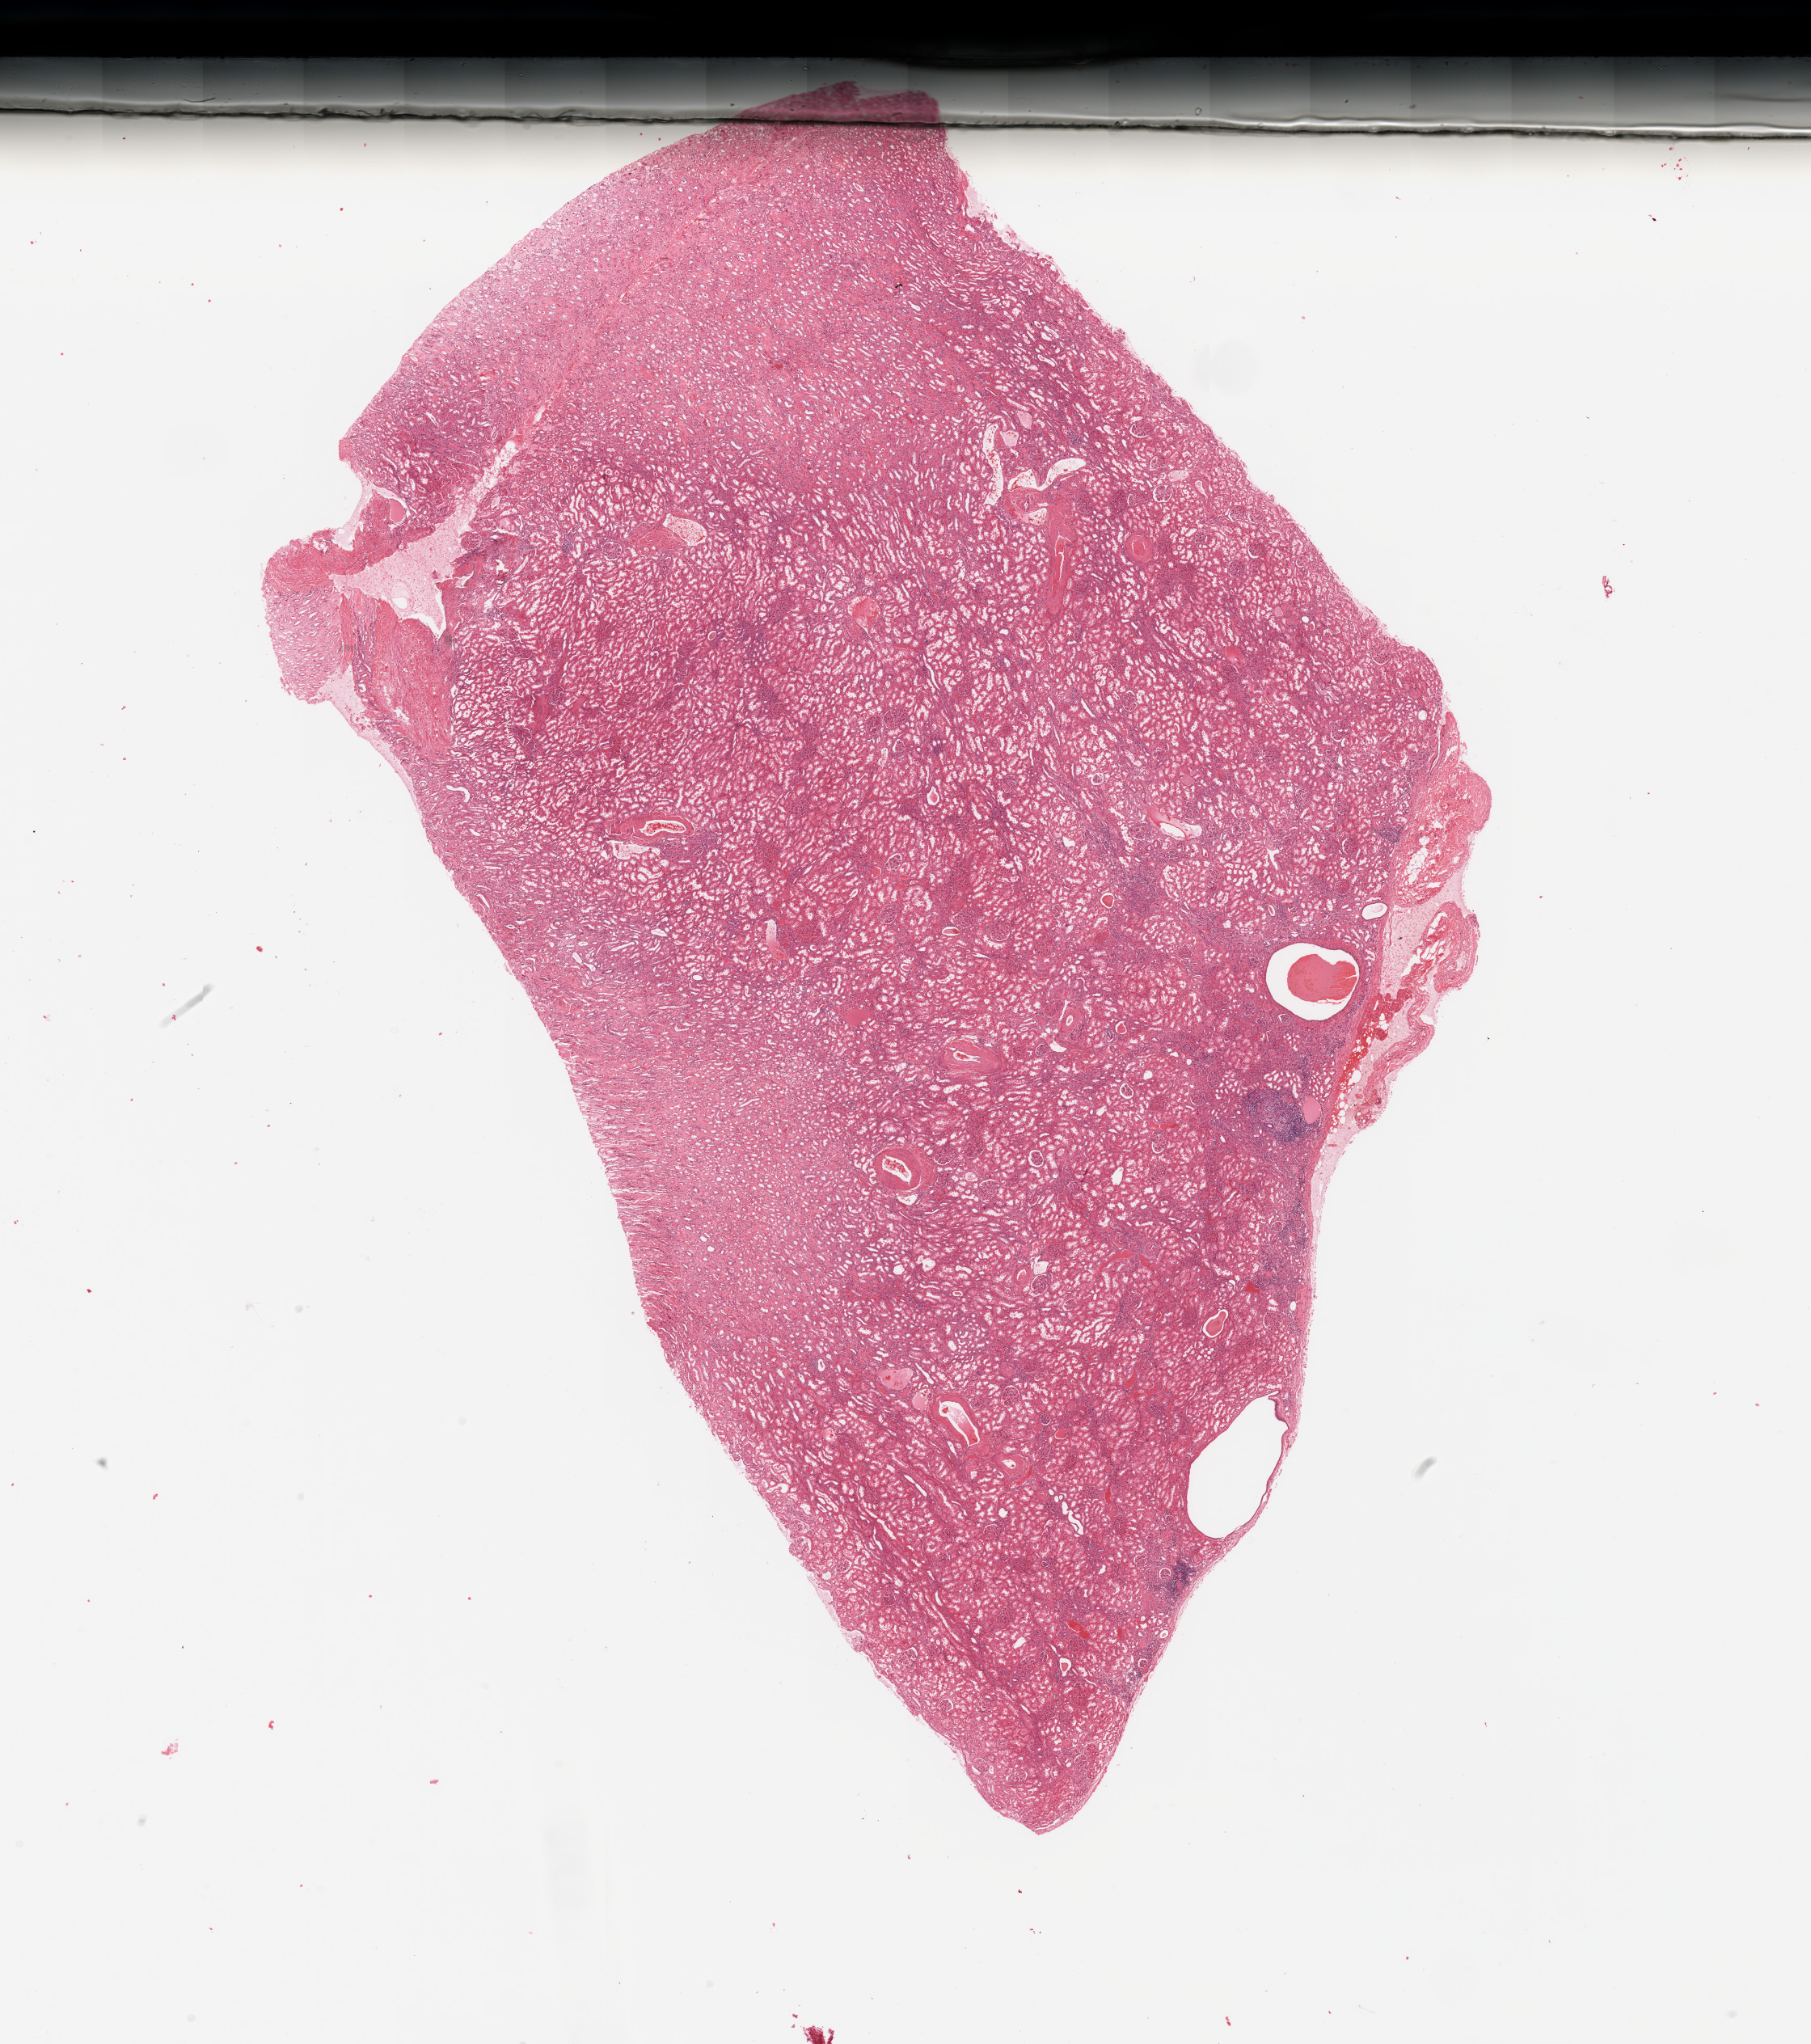
Whole-slide histology image, H&E, whole scanned area (about 17.7 x 20.0 mm) shown as a low-resolution overview; normal (non-tumour) tissue sample, kidney. Patient: male, age 72 years.
* this section: normal (non-tumour) tissue from the same patient
* patient diagnosis: Renal cell carcinoma, NOS